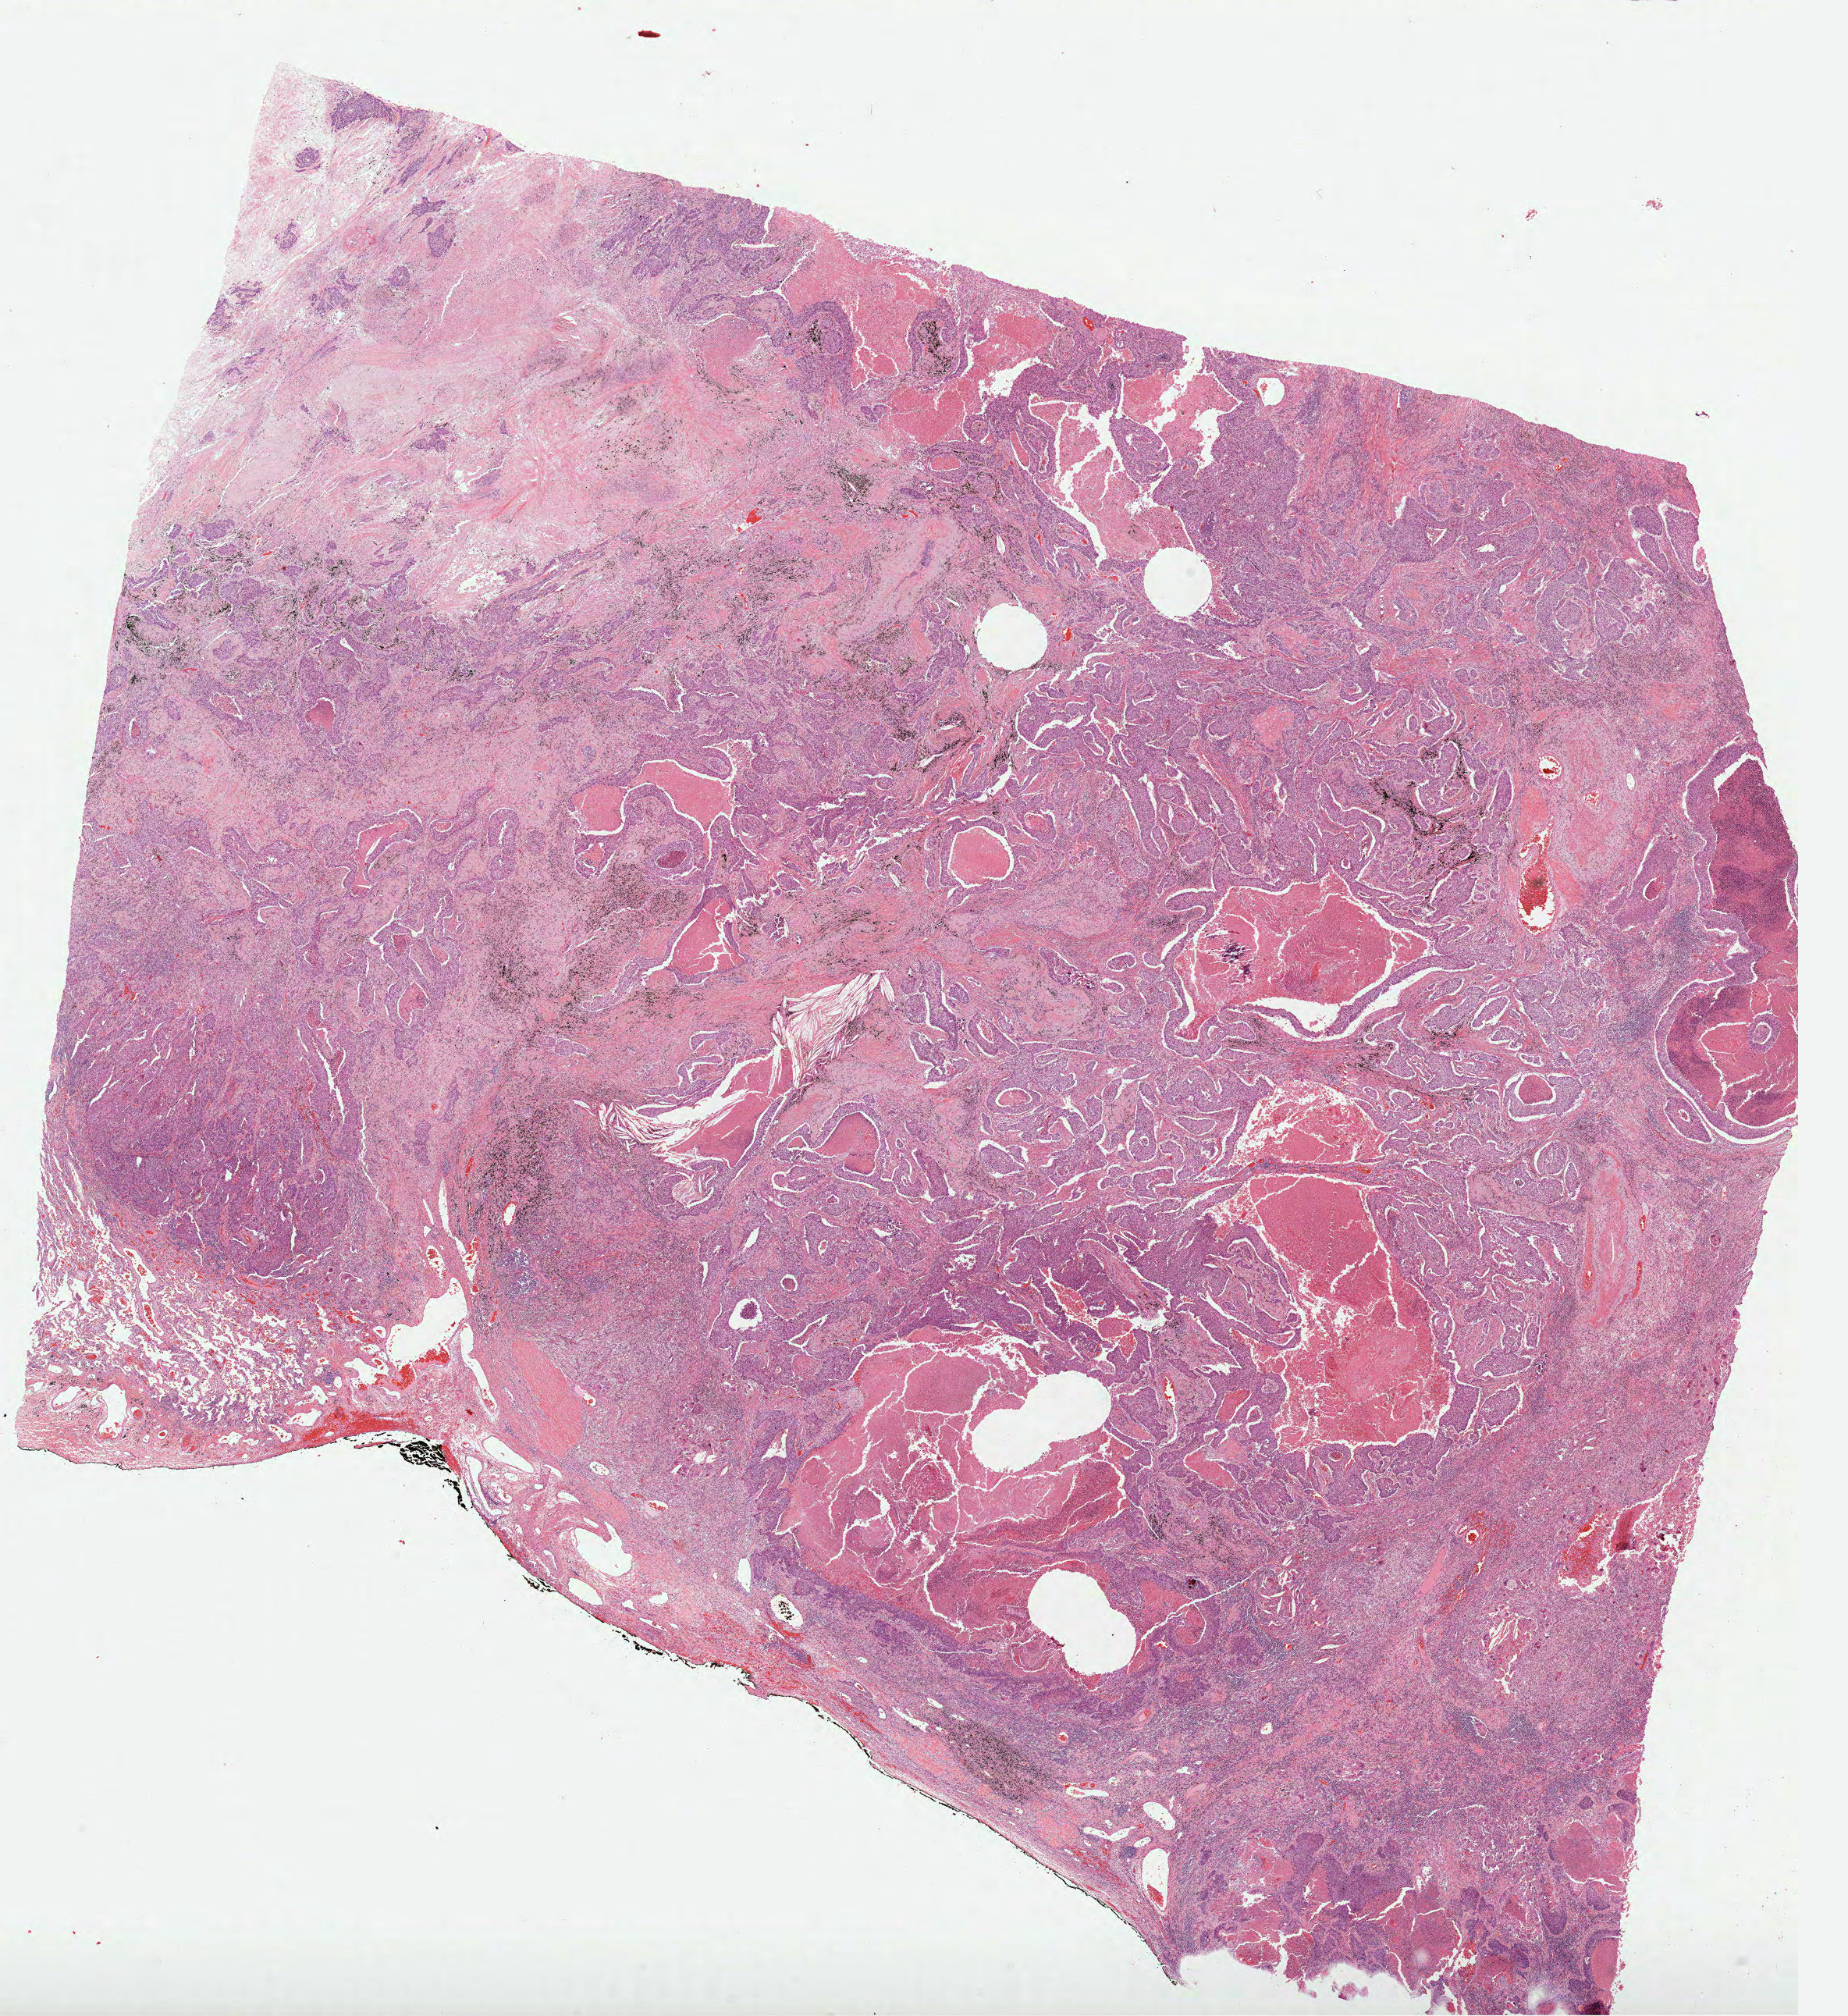
Whole-slide histology image, Hematoxylin and eosin (H&E) stained — shown as a low-resolution overview of the whole scanned area (about 19.1 x 20.8 mm, from a 40x scan), formalin-fixed paraffin-embedded (FFPE) diagnostic section, lung, primary tumour sample. Male, age 69 years at initial diagnosis.
AJCC pathologic stage: IB (6th edition). TNM: T2 N0 MX. Laterality: left. Diagnosis: Squamous cell carcinoma, NOS (upper lobe, lung).